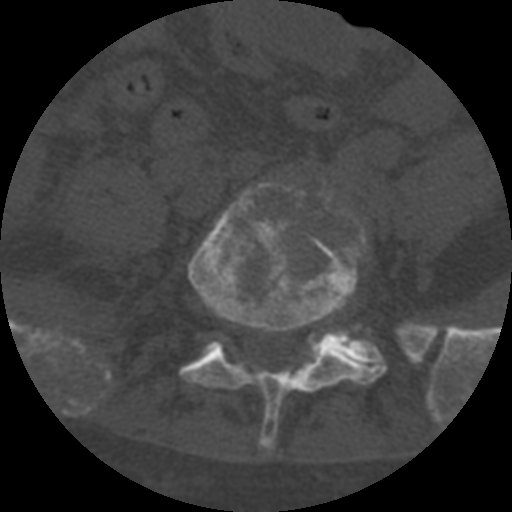
CT including the spine, one axial slice. Slice 180 of 708 in the series (ordered by position). Reconstruction kernel STANDARD. 120 kVp. One of 3 acquisitions stored at this slice position. Bone window (W 1800 / L 400 HU). 1.25 mm slice thickness. 512 × 512 image matrix. Patient age 55 years. From the clinical record (not read from this slice): primary cancer: colon.
Outlined on this slice (semi-automatically segmented with operator editing):
- L5 vertebra: box from (x=180, y=182) to (x=387, y=451) px